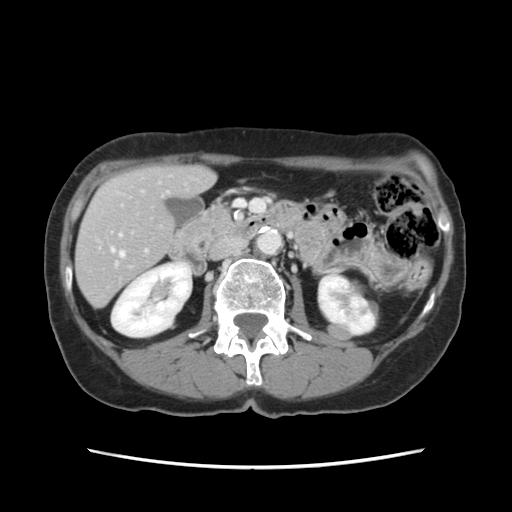
Contrast-enhanced abdominal CT, one axial slice. Slice 47 of 120 in the series (ordered by position). 120 kVp. Intravenous contrast given. Soft-tissue window (W 400 / L 40 HU). 2.5 mm slice thickness. 512 × 512 image matrix, field of view 330 × 330 mm. Female patient, age 70 years. From the clinical record (not read from this slice): diagnosis: colorectal cancer liver metastases, imaged before liver resection; multiple liver metastases: no; largest metastasis: 2.5 cm; disease in both lobes: no.
Structures marked on this image (manually delineated by an expert):
- hepatic veins: bounding box [x1, y1, x2, y2] px = [111, 248, 124, 257]
- liver: [77, 167, 214, 305]
- planned liver remnant (the part of the liver to remain after resection): [77, 167, 213, 306]
- portal vein (with intrahepatic branches): [119, 234, 147, 253]